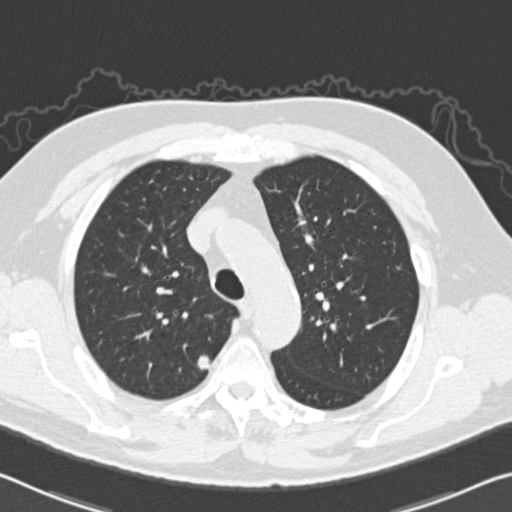
Low-dose screening chest CT, one axial slice; position 114 of 151 along the scan axis; reconstruction kernel B30f; 120 kVp; lung window (W 1500 / L -600 HU); 2 mm slice thickness; 512 × 512 image matrix, field of view 340 × 340 mm.
Outlined on this slice (manually delineated by an expert):
- lesion 1 (tumor, upper lobe of right lung): bounding box (x1, y1, x2, y2) in pixels: (197, 355, 212, 370)